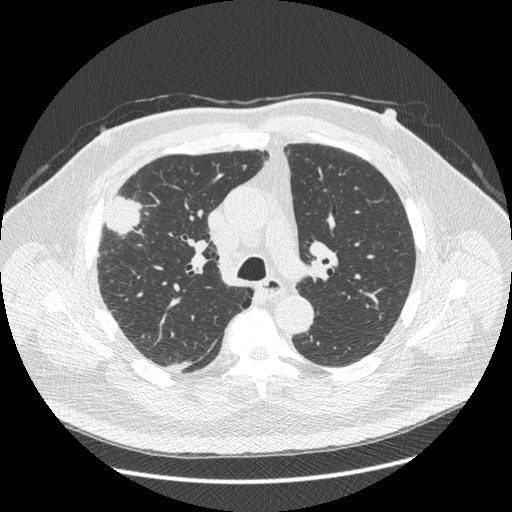
Low-dose screening chest CT, one axial slice; position 282 of 426 along the scan axis; reconstruction kernel STANDARD; 120 kVp; lung window (W 1500 / L -600 HU); 1.25 mm slice thickness; 512 × 512 image matrix.
Annotated regions visible in this slice (expert manual segmentation):
- lesion 1 (tumor, upper lobe of right lung): bounding box <106,196,140,235> (left, top, right, bottom; pixels)